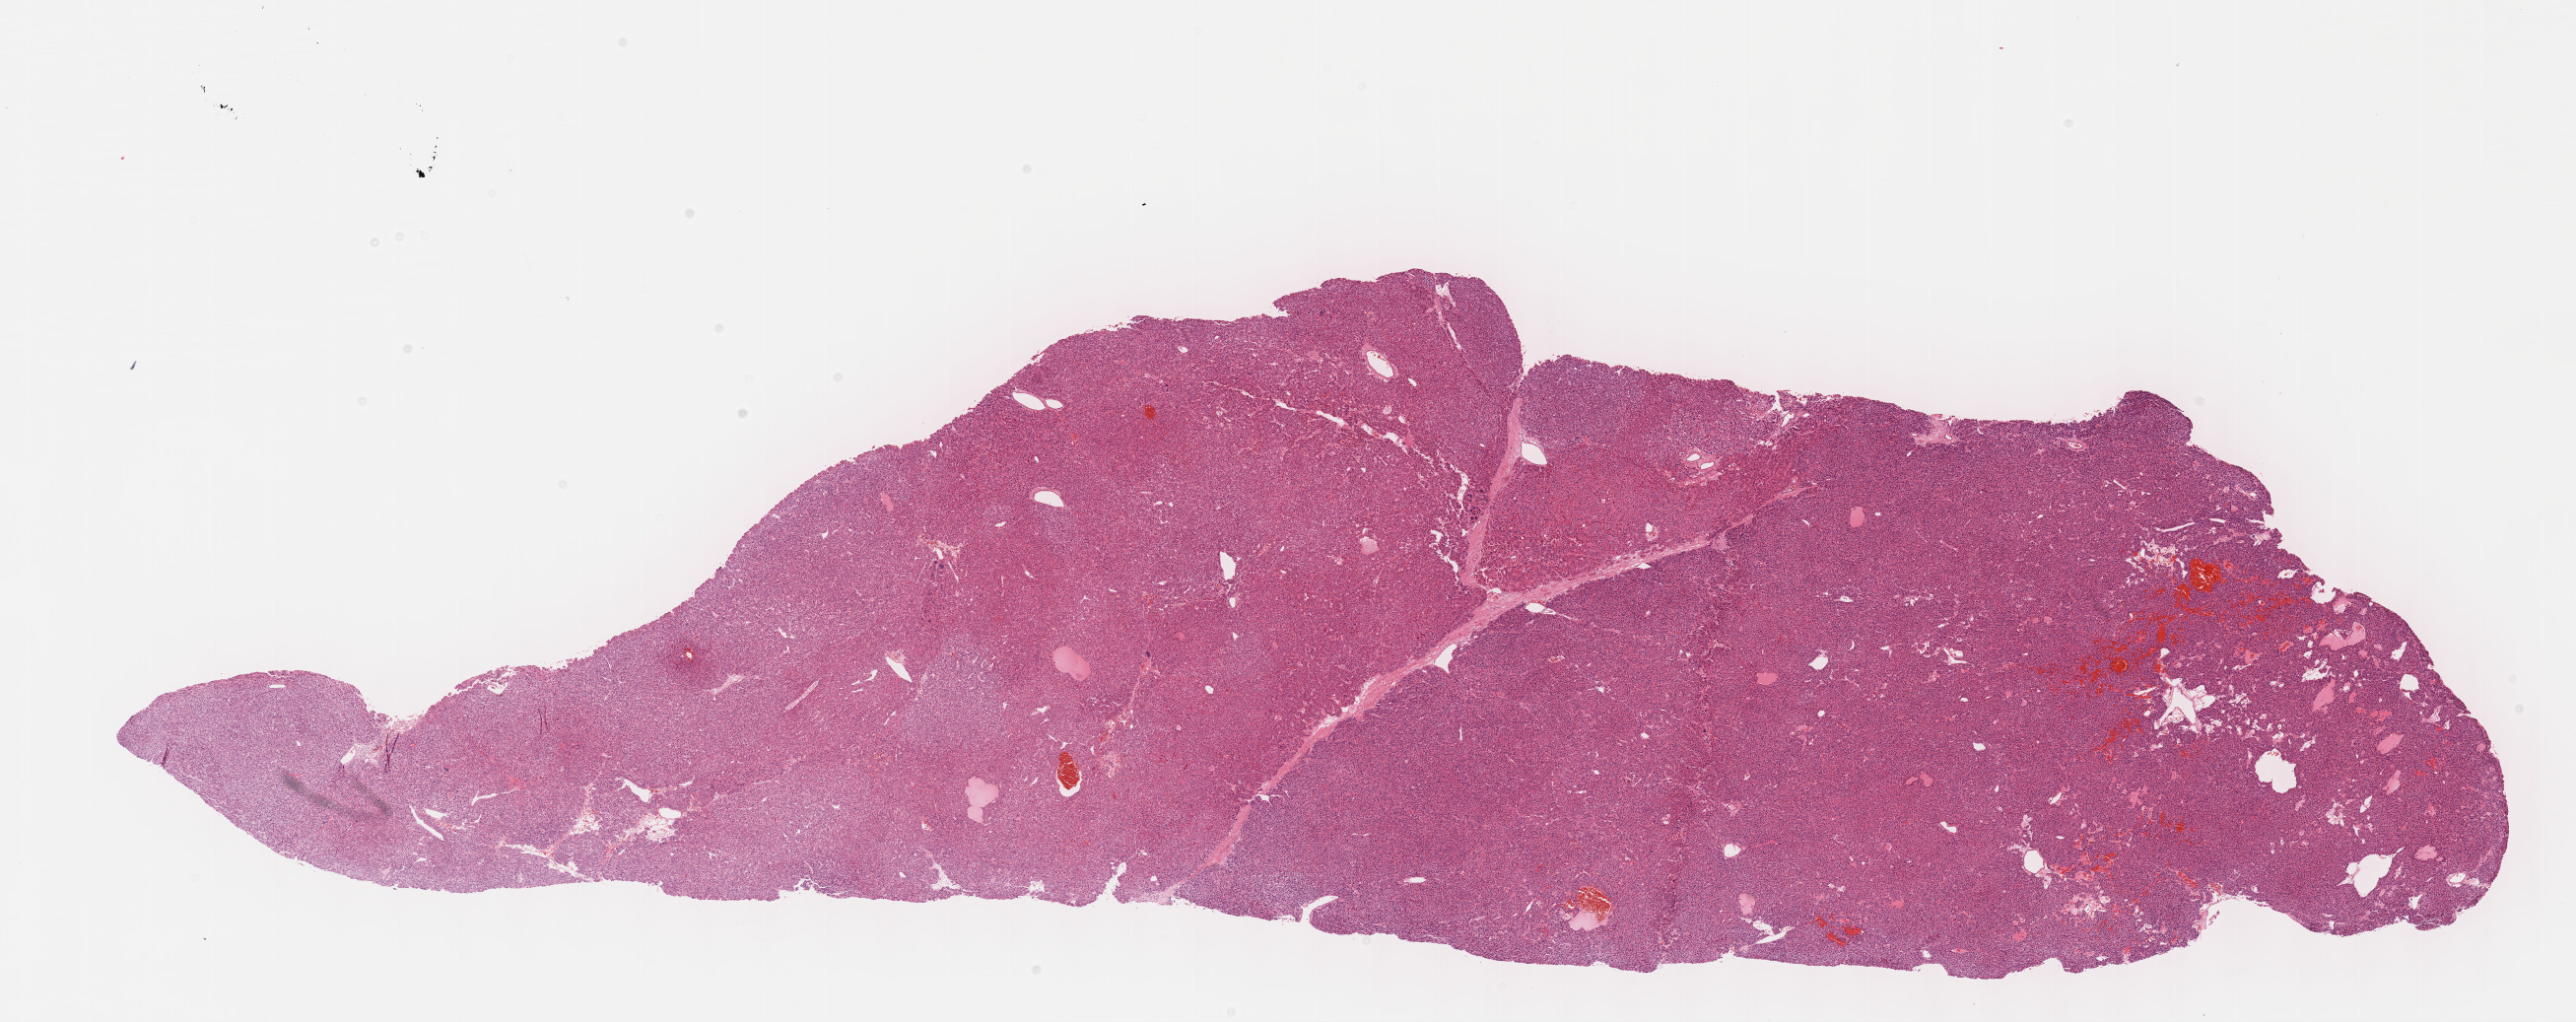
Whole-slide histology image, H&E-stained, whole scanned area (about 21.1 x 8.4 mm, acquisition: 40x scan) shown as a low-resolution overview, formalin-fixed paraffin-embedded (FFPE) diagnostic section, primary tumour sample from the liver. Patient: male, age at initial diagnosis 53 years.
Pathologic diagnosis: Hepatocellular carcinoma, NOS.